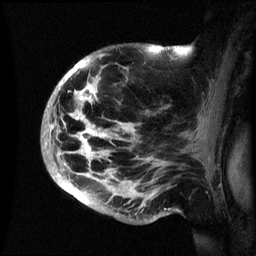
Breast MRI (dynamic contrast-enhanced), one sagittal slice; position 41 of 60 along the scan axis; dynamic contrast-enhanced series, image 2 of 3 at this slice position (ordered by acquisition); 1.5 T; TE 4.2 ms, TR 8.4 ms; 2.4 mm slice thickness; 256 × 256 image matrix, field of view 230 × 230 mm. Patient: female, 48 years.
Annotated regions visible in this slice (semi-automatic segmentation, software-assisted and operator-edited):
- analysis volume of interest (the breast-tissue region the enhancement analysis was run in; not a lesion): bounding box (x1, y1, x2, y2) in pixels: (42, 45, 193, 222)
- tumour enhancement mask (voxels above the 70 % enhancement threshold inside the analysis volume of interest): (45, 47, 154, 194)